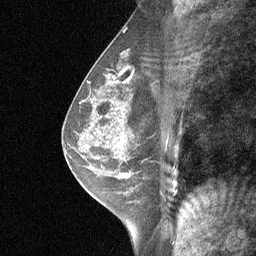
Breast MRI (dynamic contrast-enhanced), one sagittal slice; slice 33 of 64 in the series (ordered by position); dynamic contrast-enhanced study with each time point stored as its own series, time point 2 of 3 at this slice position (early post-contrast, ordered by acquisition time); 1.5 T; TE 4.8 ms, TR 27 ms; 2 mm slice thickness; 256 × 256 image matrix, field of view 180 × 180 mm. Patient: female, 47 years. Case-level facts recorded for this patient, not image findings: setting: breast cancer imaged before/during neoadjuvant chemotherapy; receptor status: HR-positive, HER2-negative.
Structures marked on this image (semi-automatic segmentation, software-assisted and operator-edited):
- analysis volume of interest (the breast-tissue region the enhancement analysis was run in; not a lesion): bounding box [x1, y1, x2, y2] px = [104, 138, 165, 198]
- tumour enhancement mask (voxels above the 90 % enhancement threshold inside the analysis volume of interest): [118, 141, 131, 178]